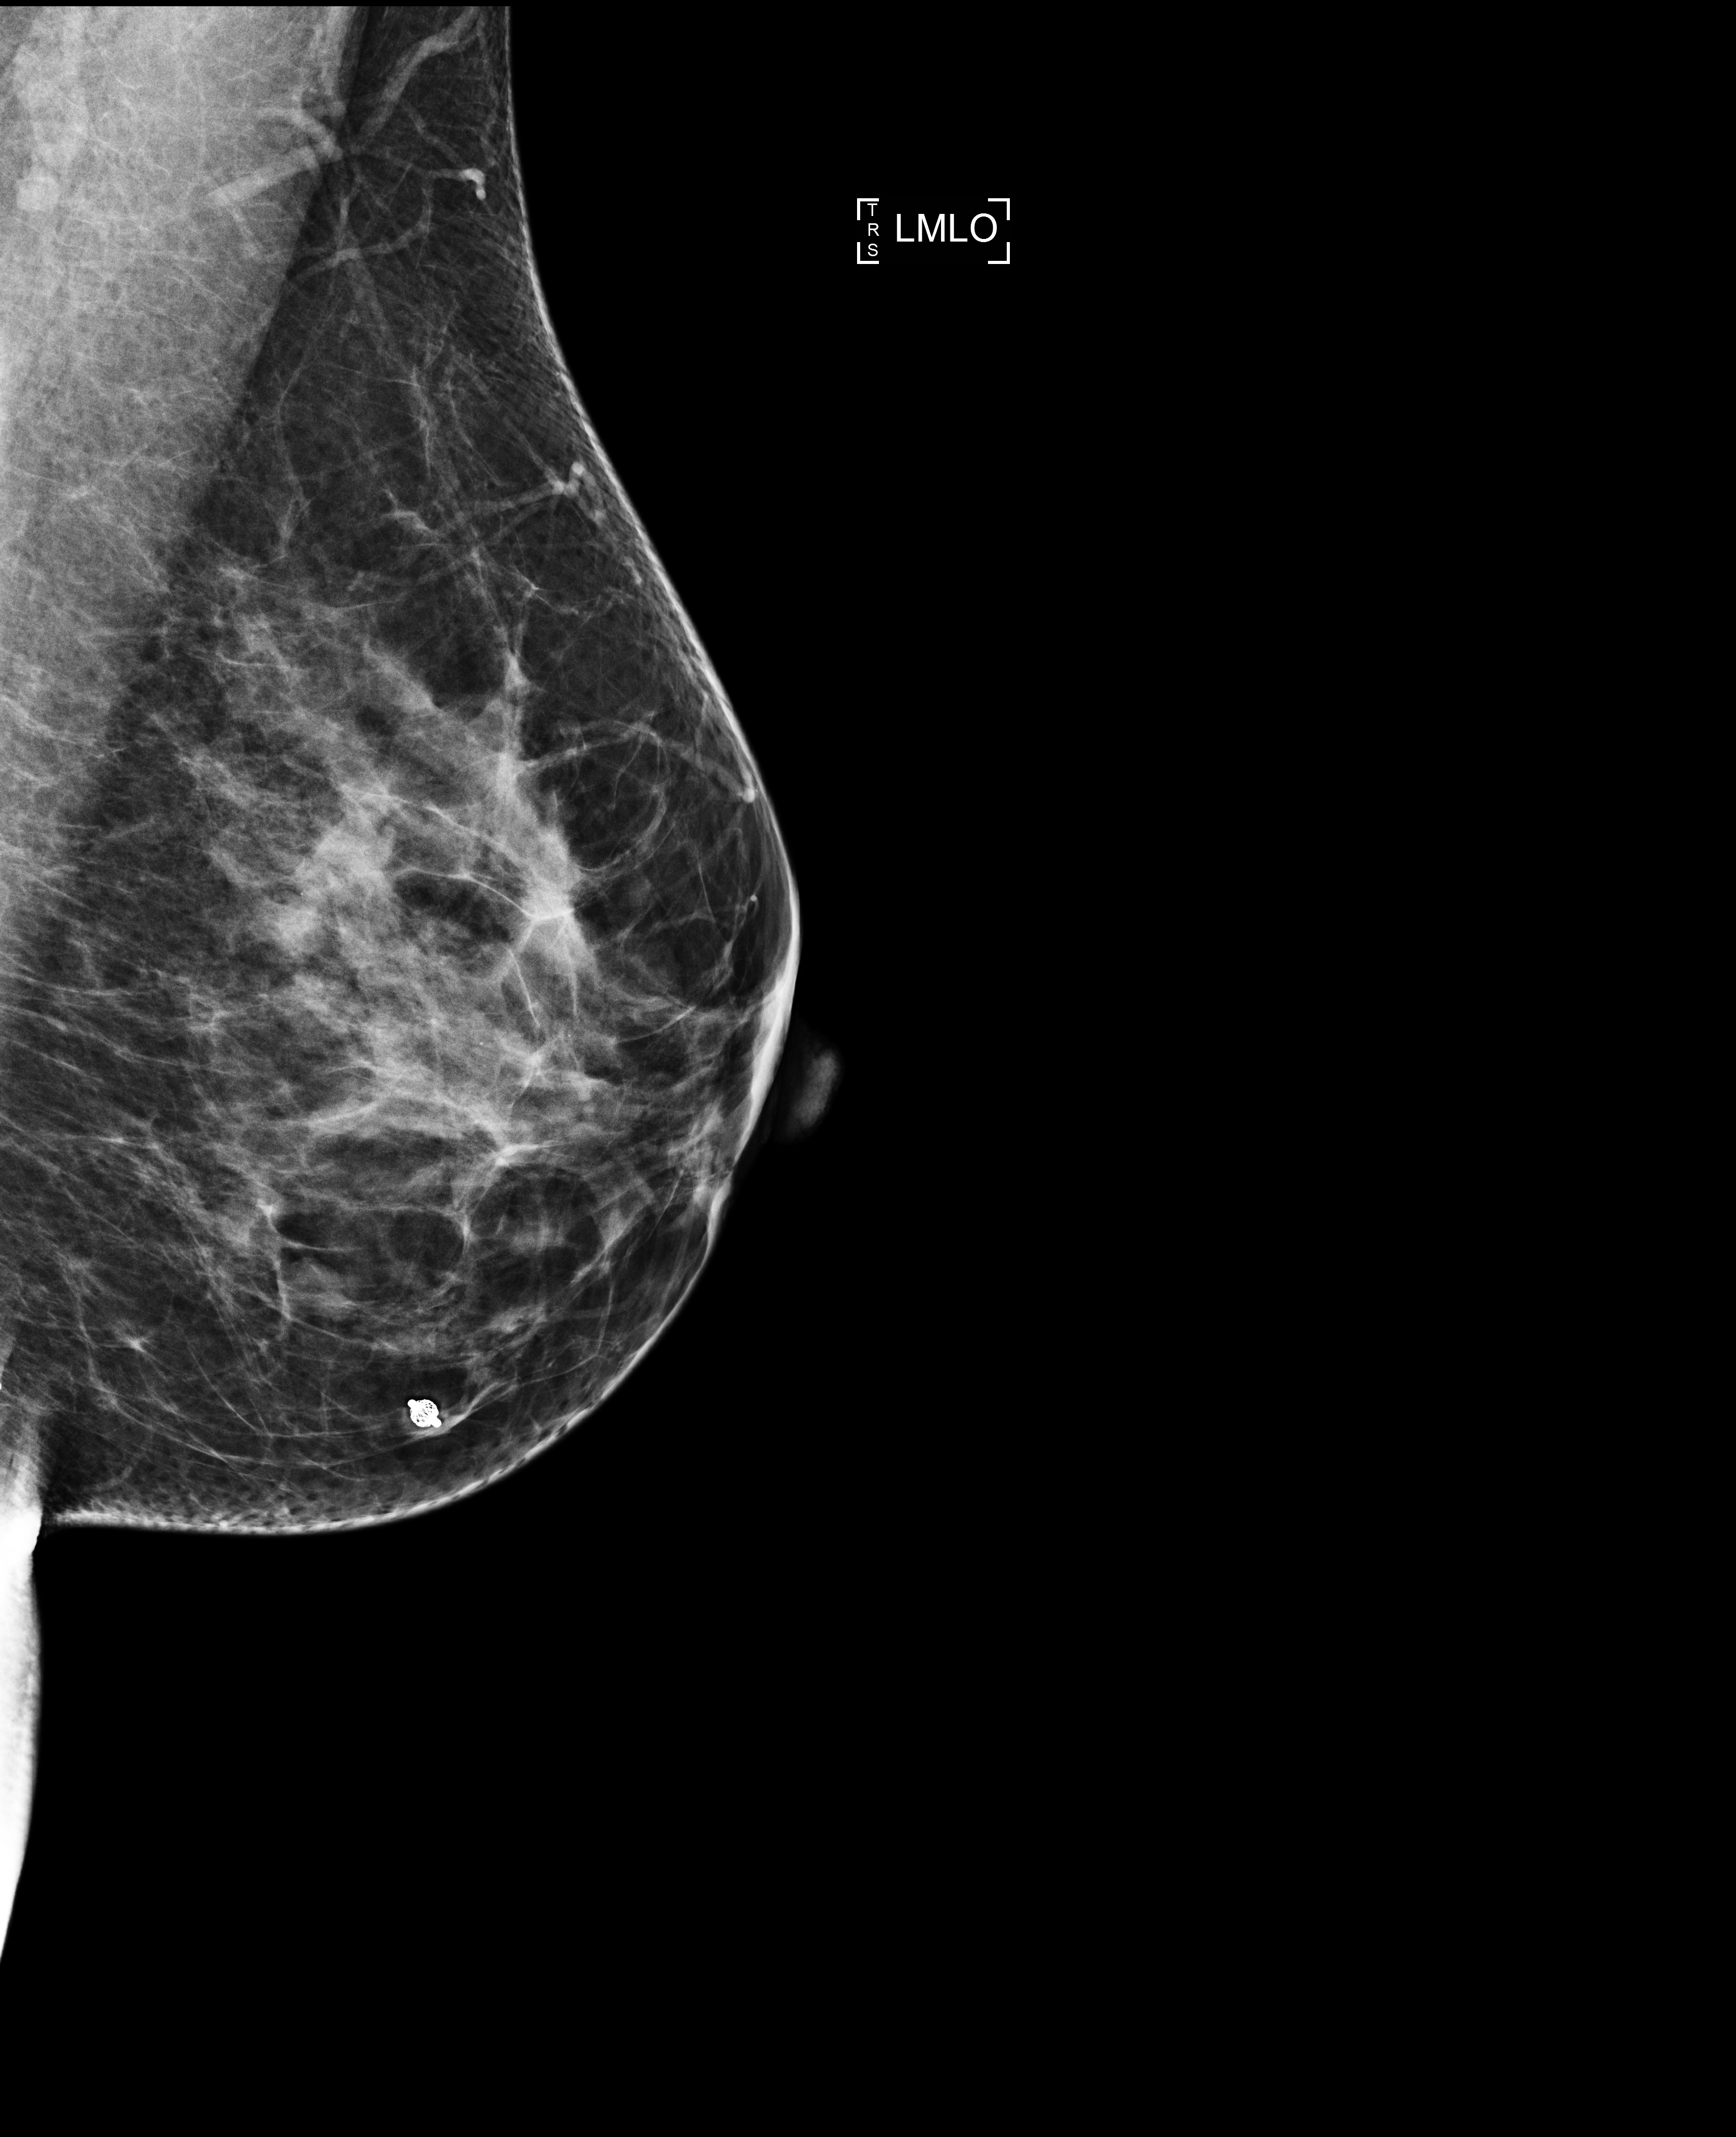
Screening examination. Patient: female, 42 years.
Image type: full-field digital mammogram. Breast: left. Projection: medio-lateral oblique projection.